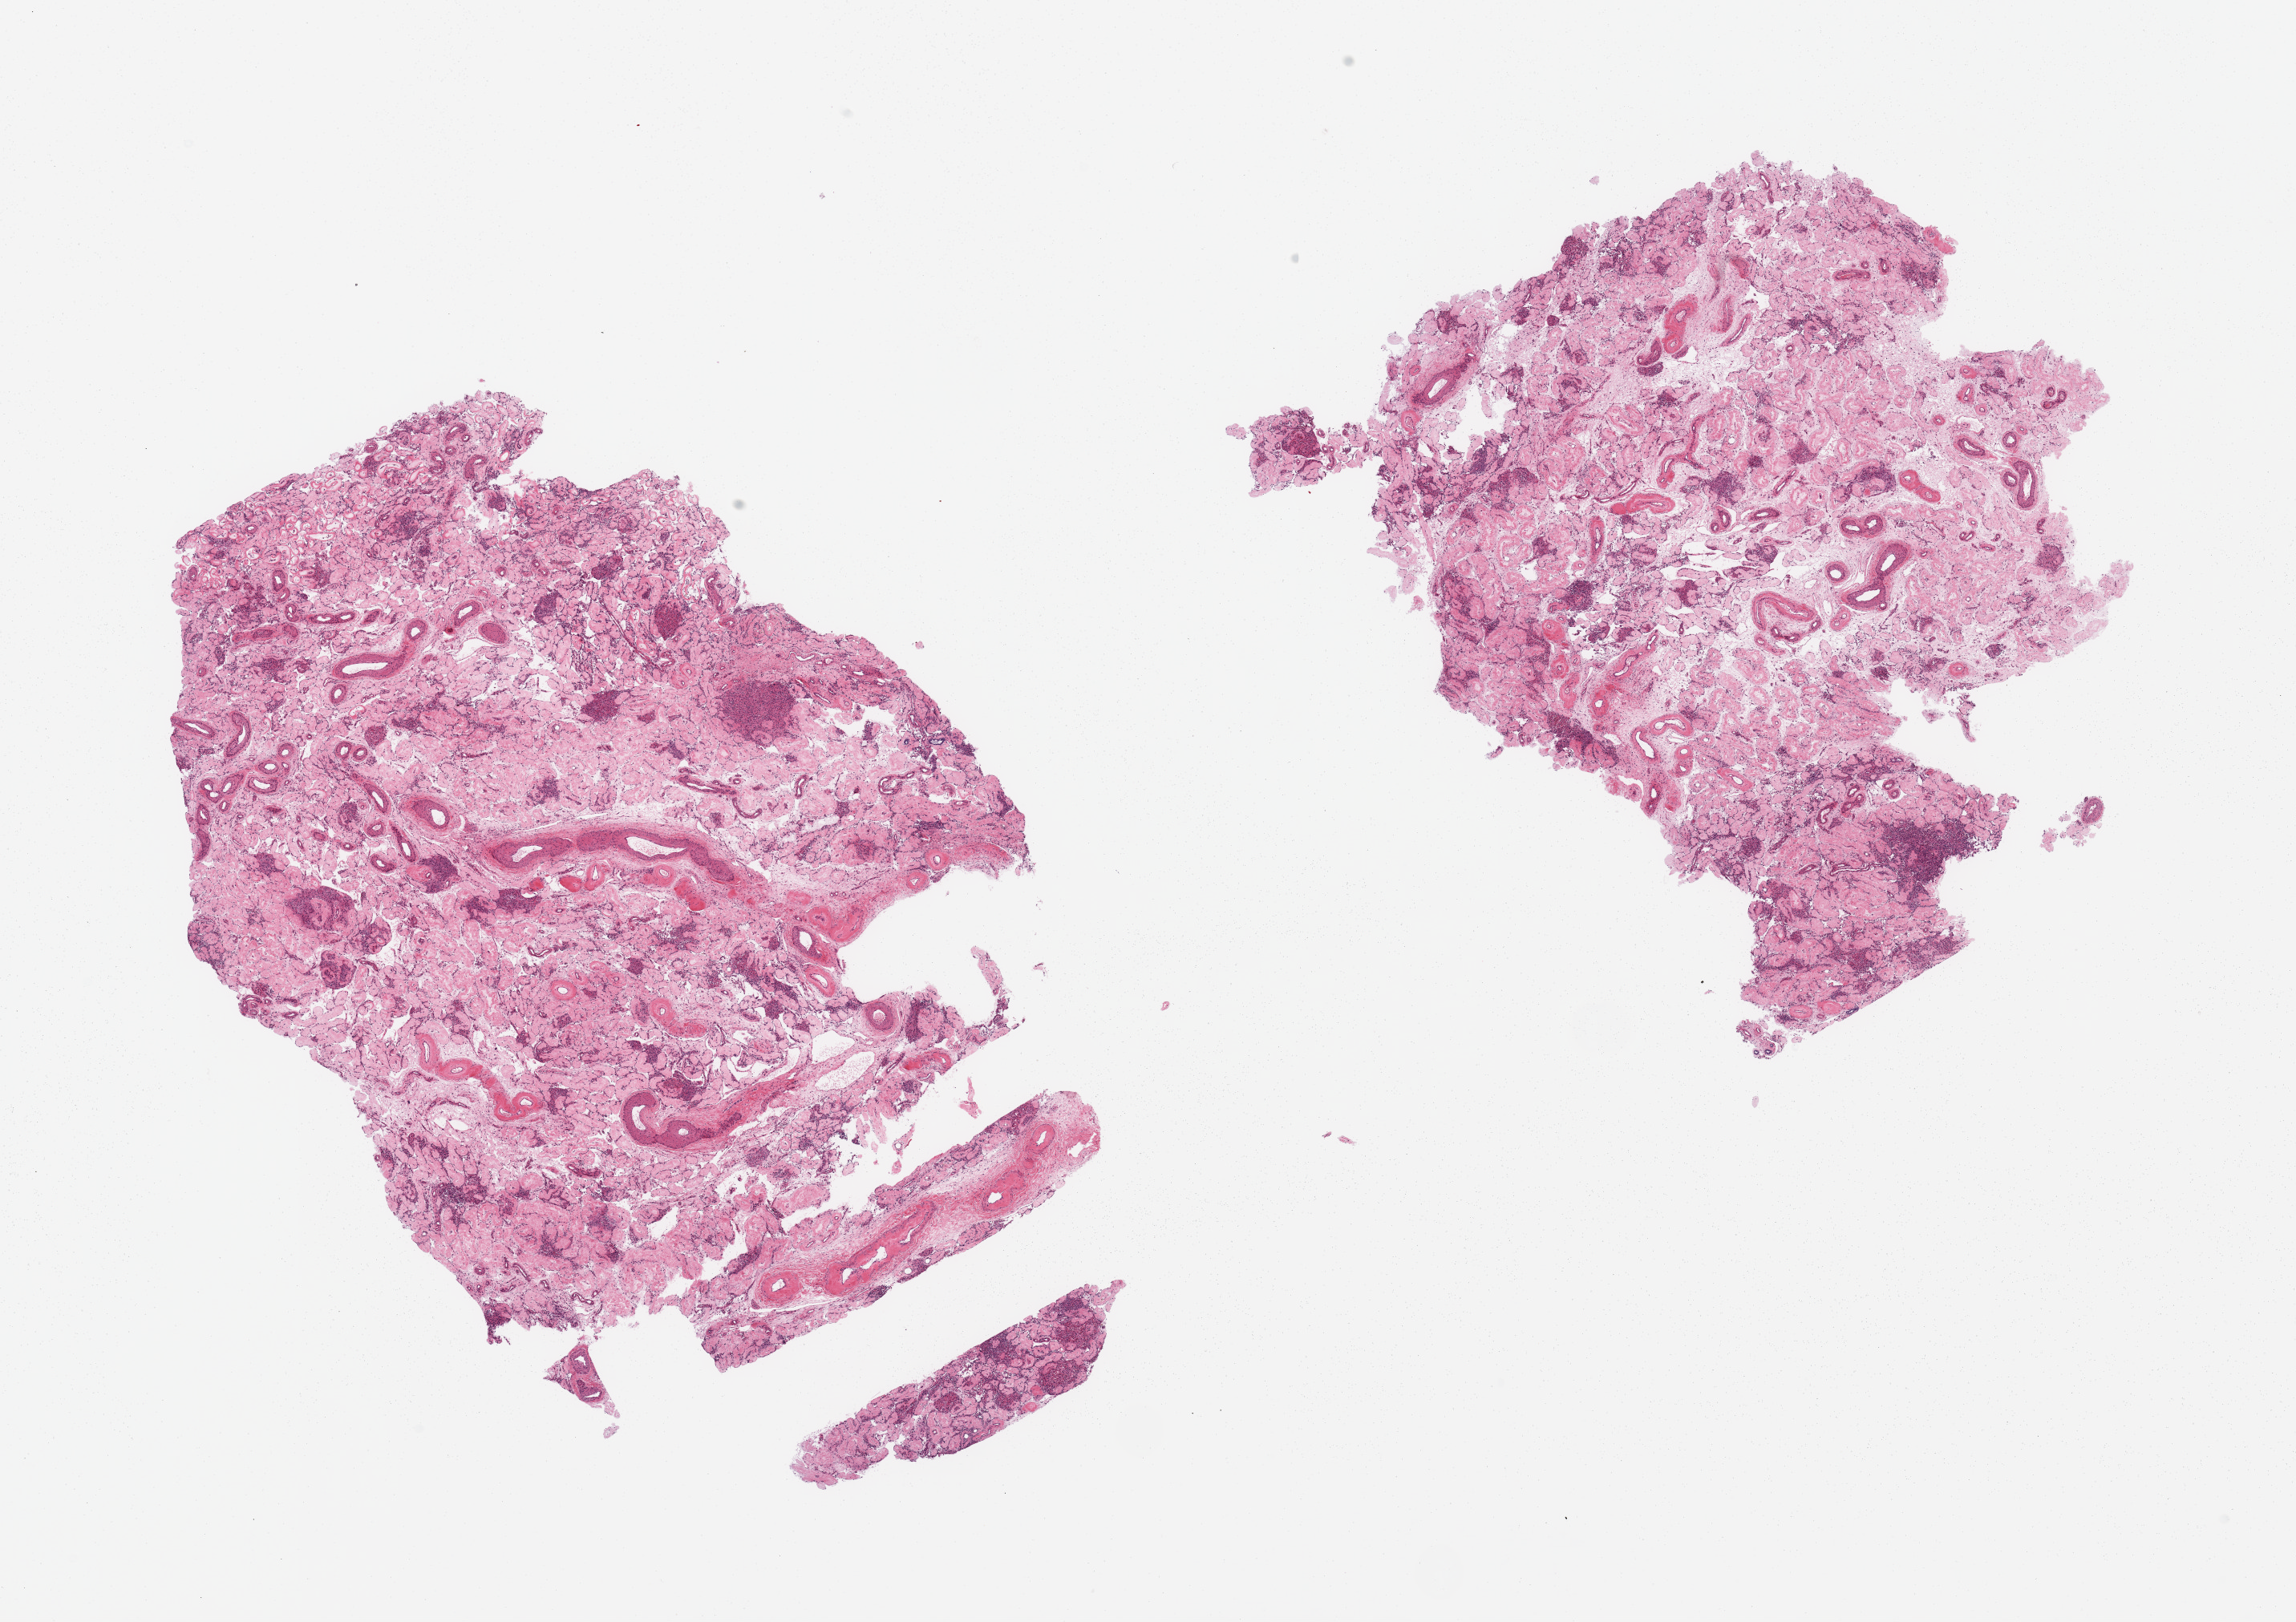
Digitized haematoxylin and eosin-stained section — low-resolution overview of the scanned area, about 22.6 x 16.0 mm (from a 20x scan), PAXgene-fixed, paraffin-embedded tissue, section of testis (target tissue), donor tissue sample. Male donor.
Reviewer comment on this tissue sample: 2 pieces; total sclerosis of tubules (no spermatogenesis) with Leydig cell hyperplasia. Changes consistent with Klinefelter syndrome.